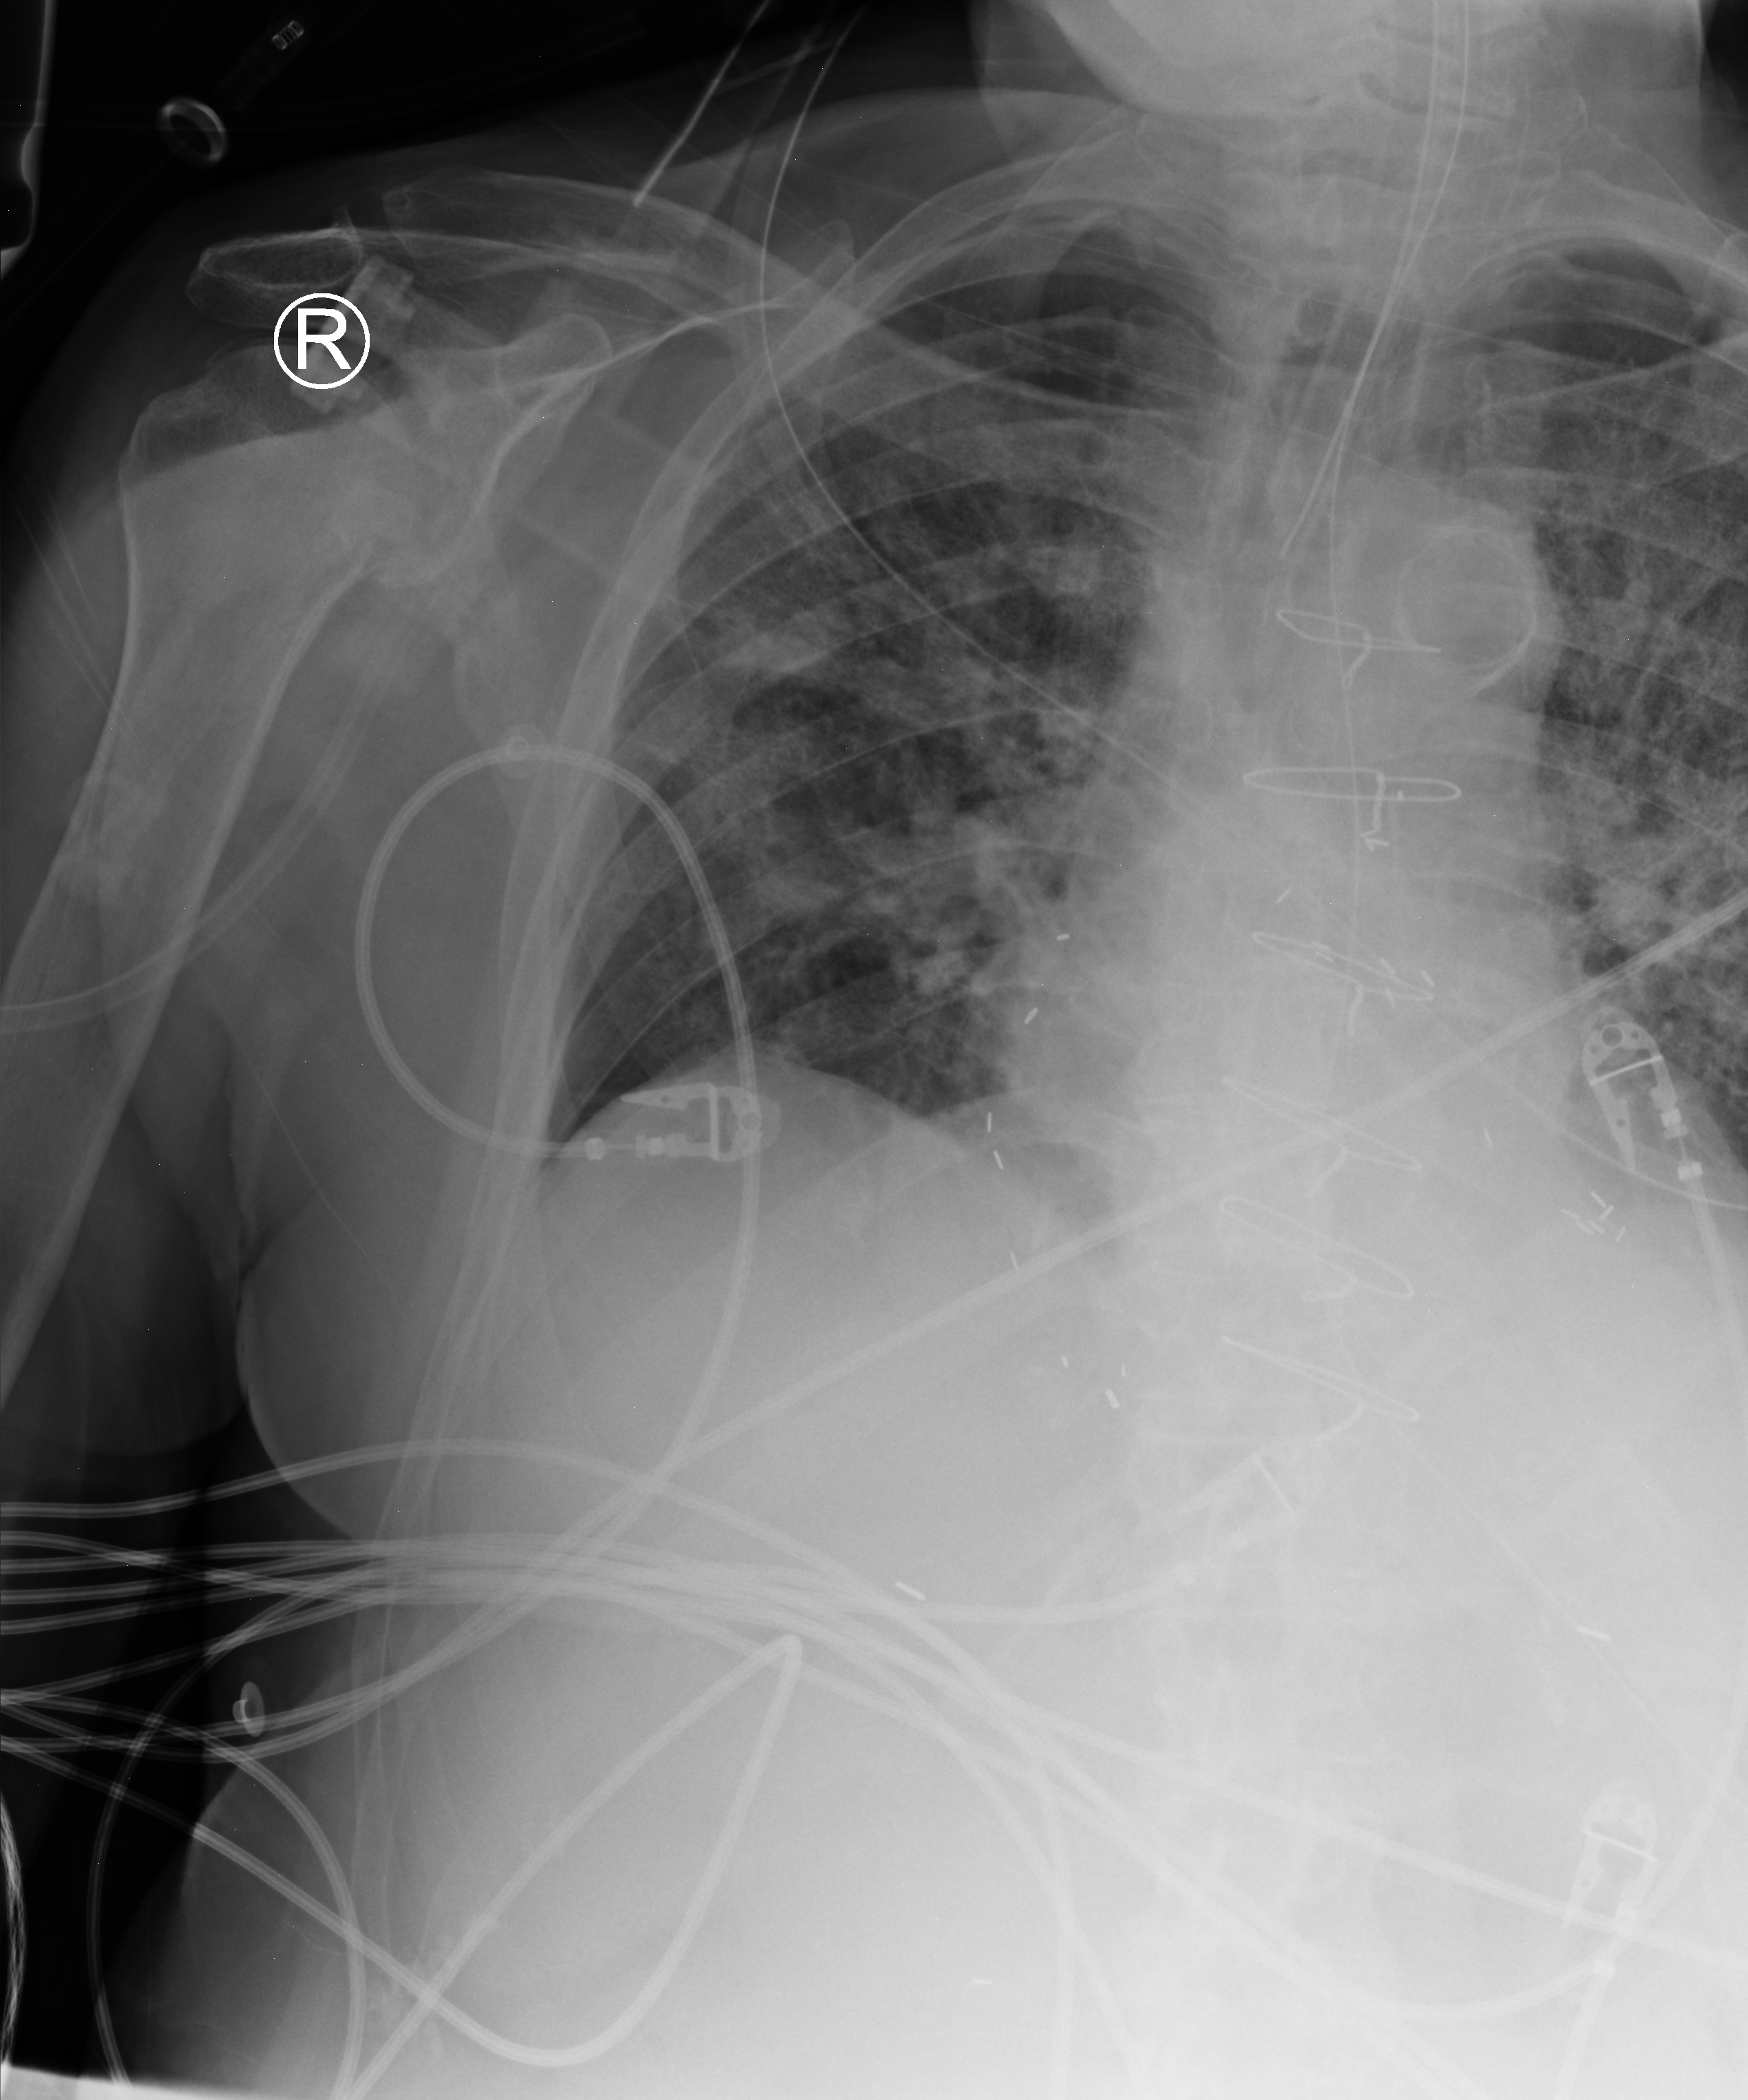
Chest X-ray (portable), anteroposterior (AP) projection. Male patient hospitalised with COVID-19, age 75–90 years.
From the hospital-stay record, not from the radiograph (when in the stay this image was taken is not recorded): mechanically ventilated during this hospital stay: yes; admitted to intensive care during this hospital stay: yes.